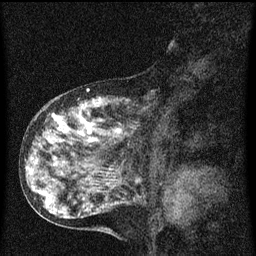
Breast MRI (dynamic contrast-enhanced), one sagittal slice. Position 27 of 60 along the scan axis. Dynamic contrast-enhanced series, image 2 of 3 at this slice position (ordered by acquisition). 1.5 T. TE 4.2 ms, TR 8 ms. 2 mm slice thickness. 256 × 256 image matrix, field of view 180 × 180 mm. Female patient, age 55 years.
Structures marked on this image (semi-automatically segmented with operator editing):
- analysis volume of interest (the breast-tissue region the enhancement analysis was run in; not a lesion): box from (x=38, y=92) to (x=175, y=159) px
- tumour enhancement mask (voxels above the 70 % enhancement threshold inside the analysis volume of interest): (x=50, y=114)–(x=123, y=143)